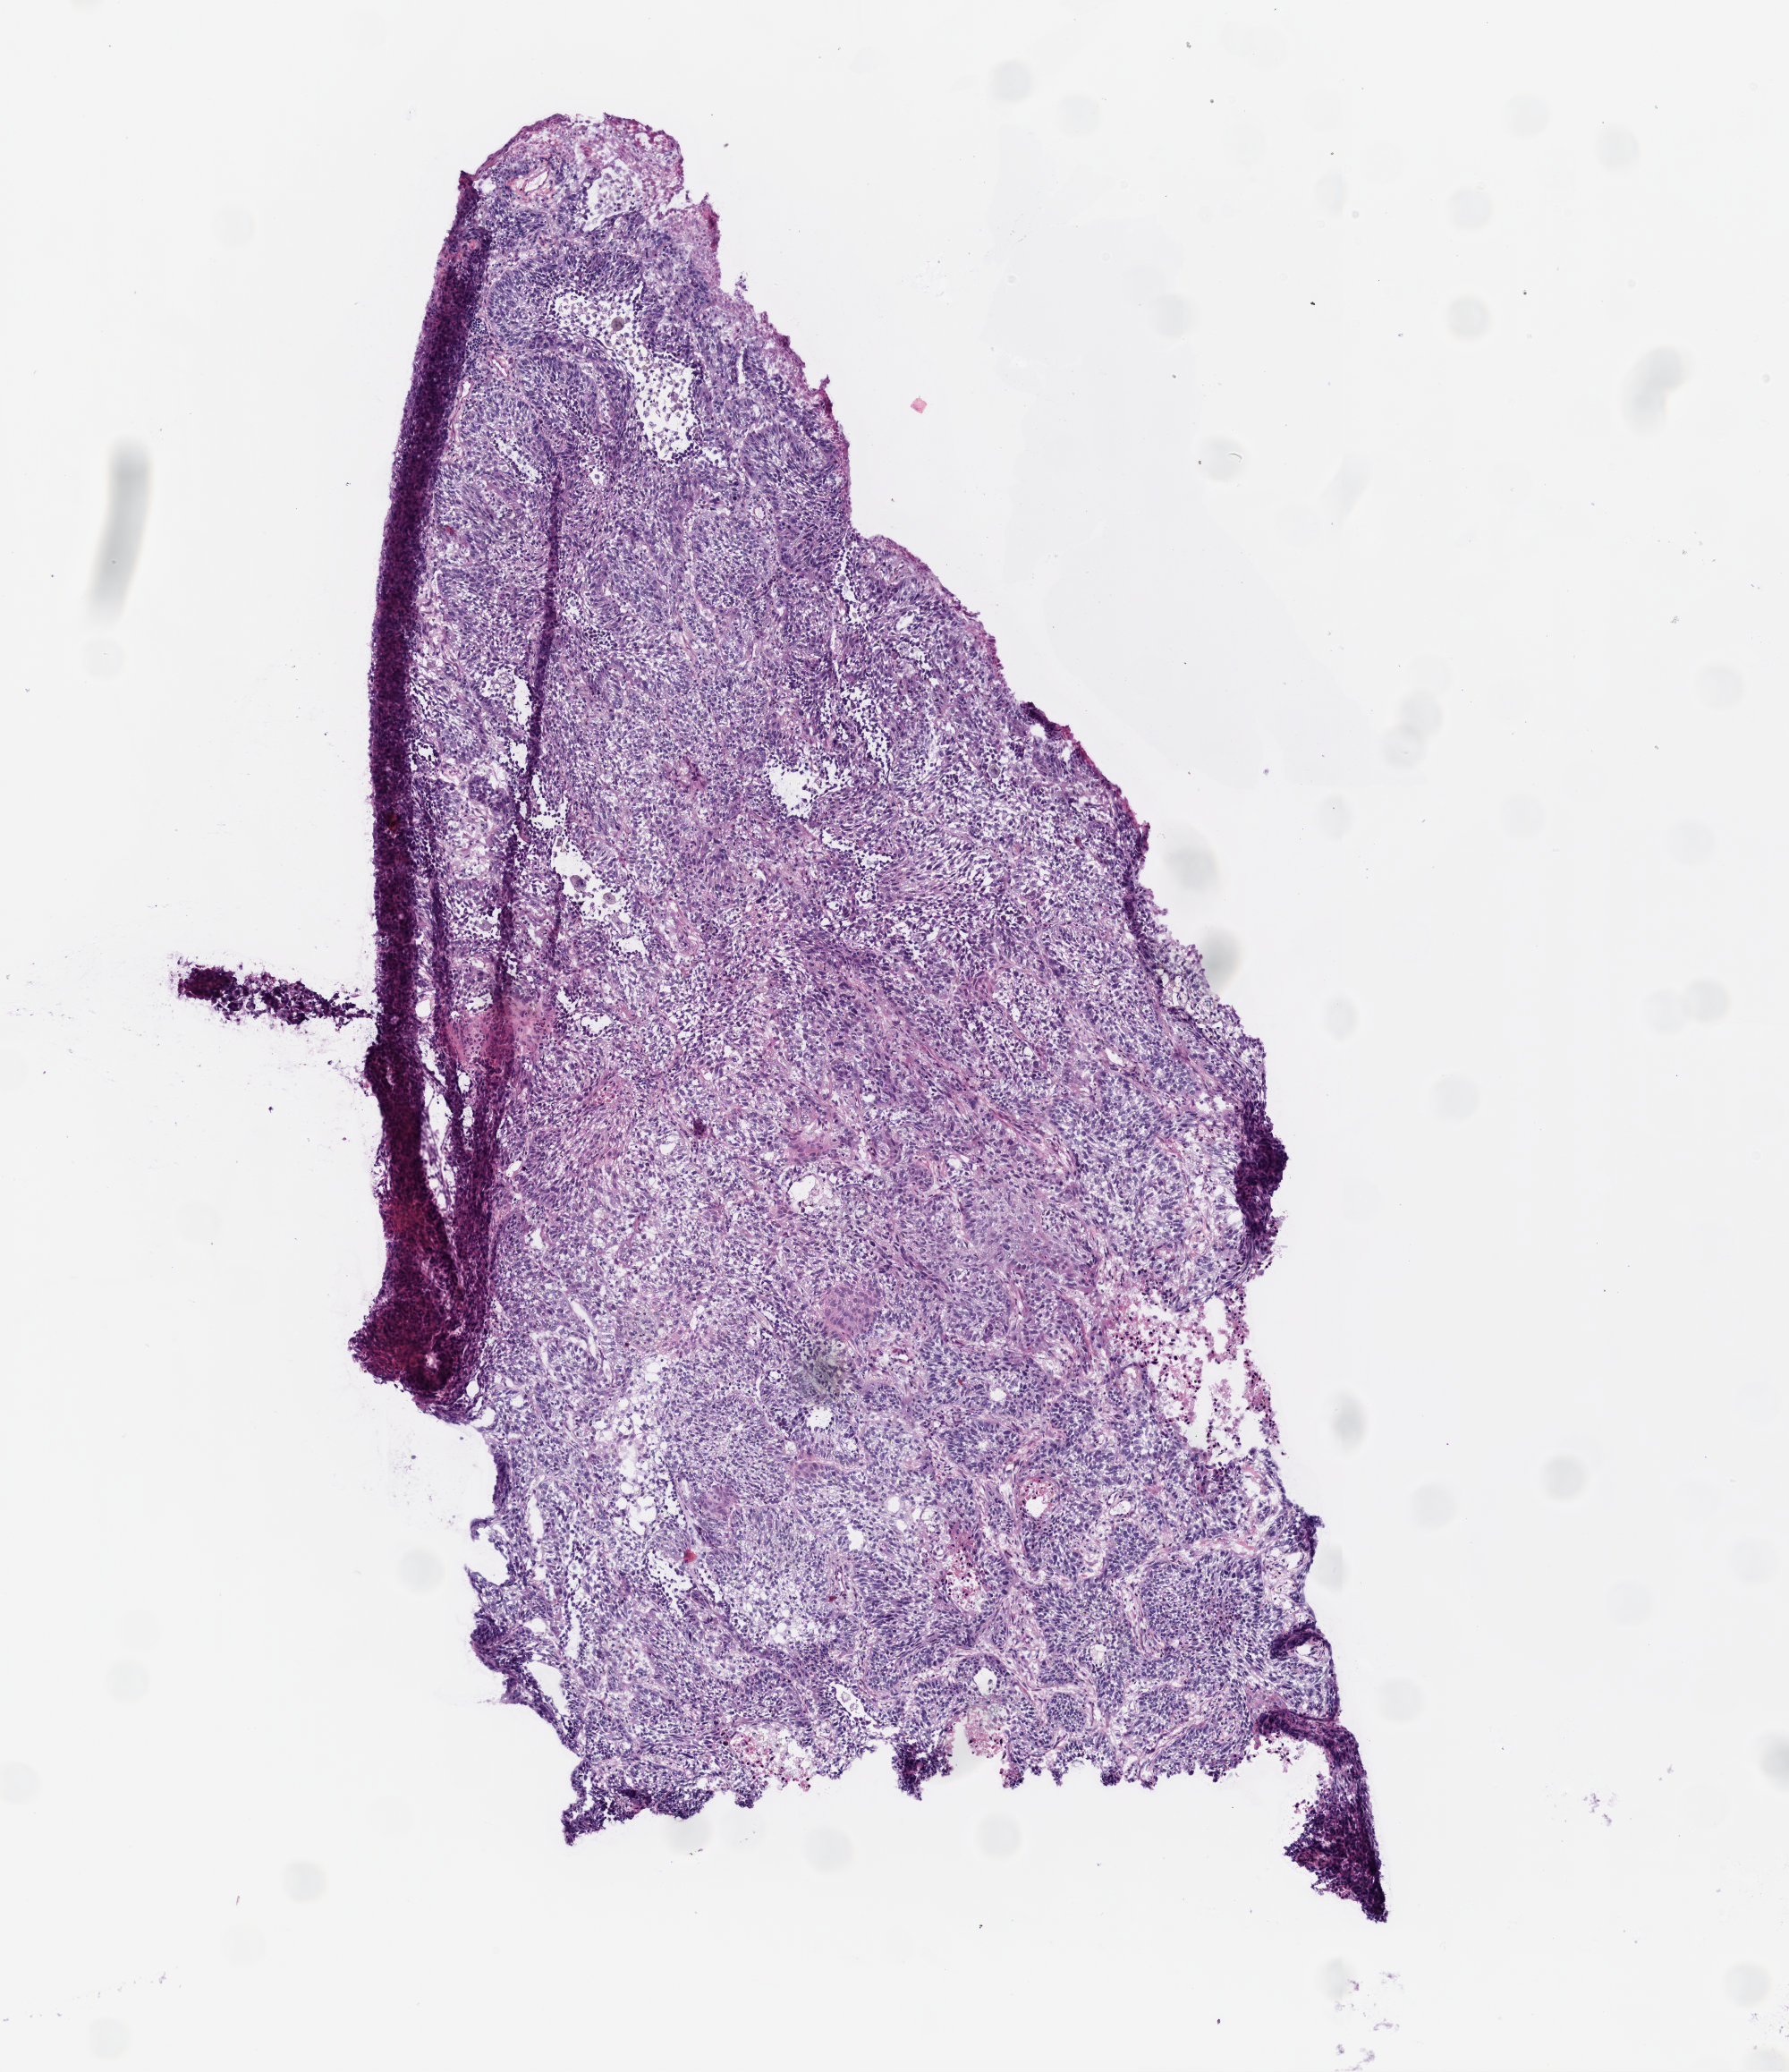
Hematoxylin and eosin (H&E) stained whole-slide image, a low-resolution overview of the entire scanned area, about 4.0 x 4.6 mm (acquisition: 20x scan), frozen section, sample: primary tumour, lung. Patient: female, age at initial diagnosis 77 years. Pathologist review of this section (percent, as recorded): tumour cells 90%, tumour nuclei 90%, normal cells 0%, stromal cells 8%, necrosis 2%.
AJCC pathologic stage: IB. Laterality: right. Pathologic diagnosis: Squamous cell carcinoma, NOS (lower lobe, lung).